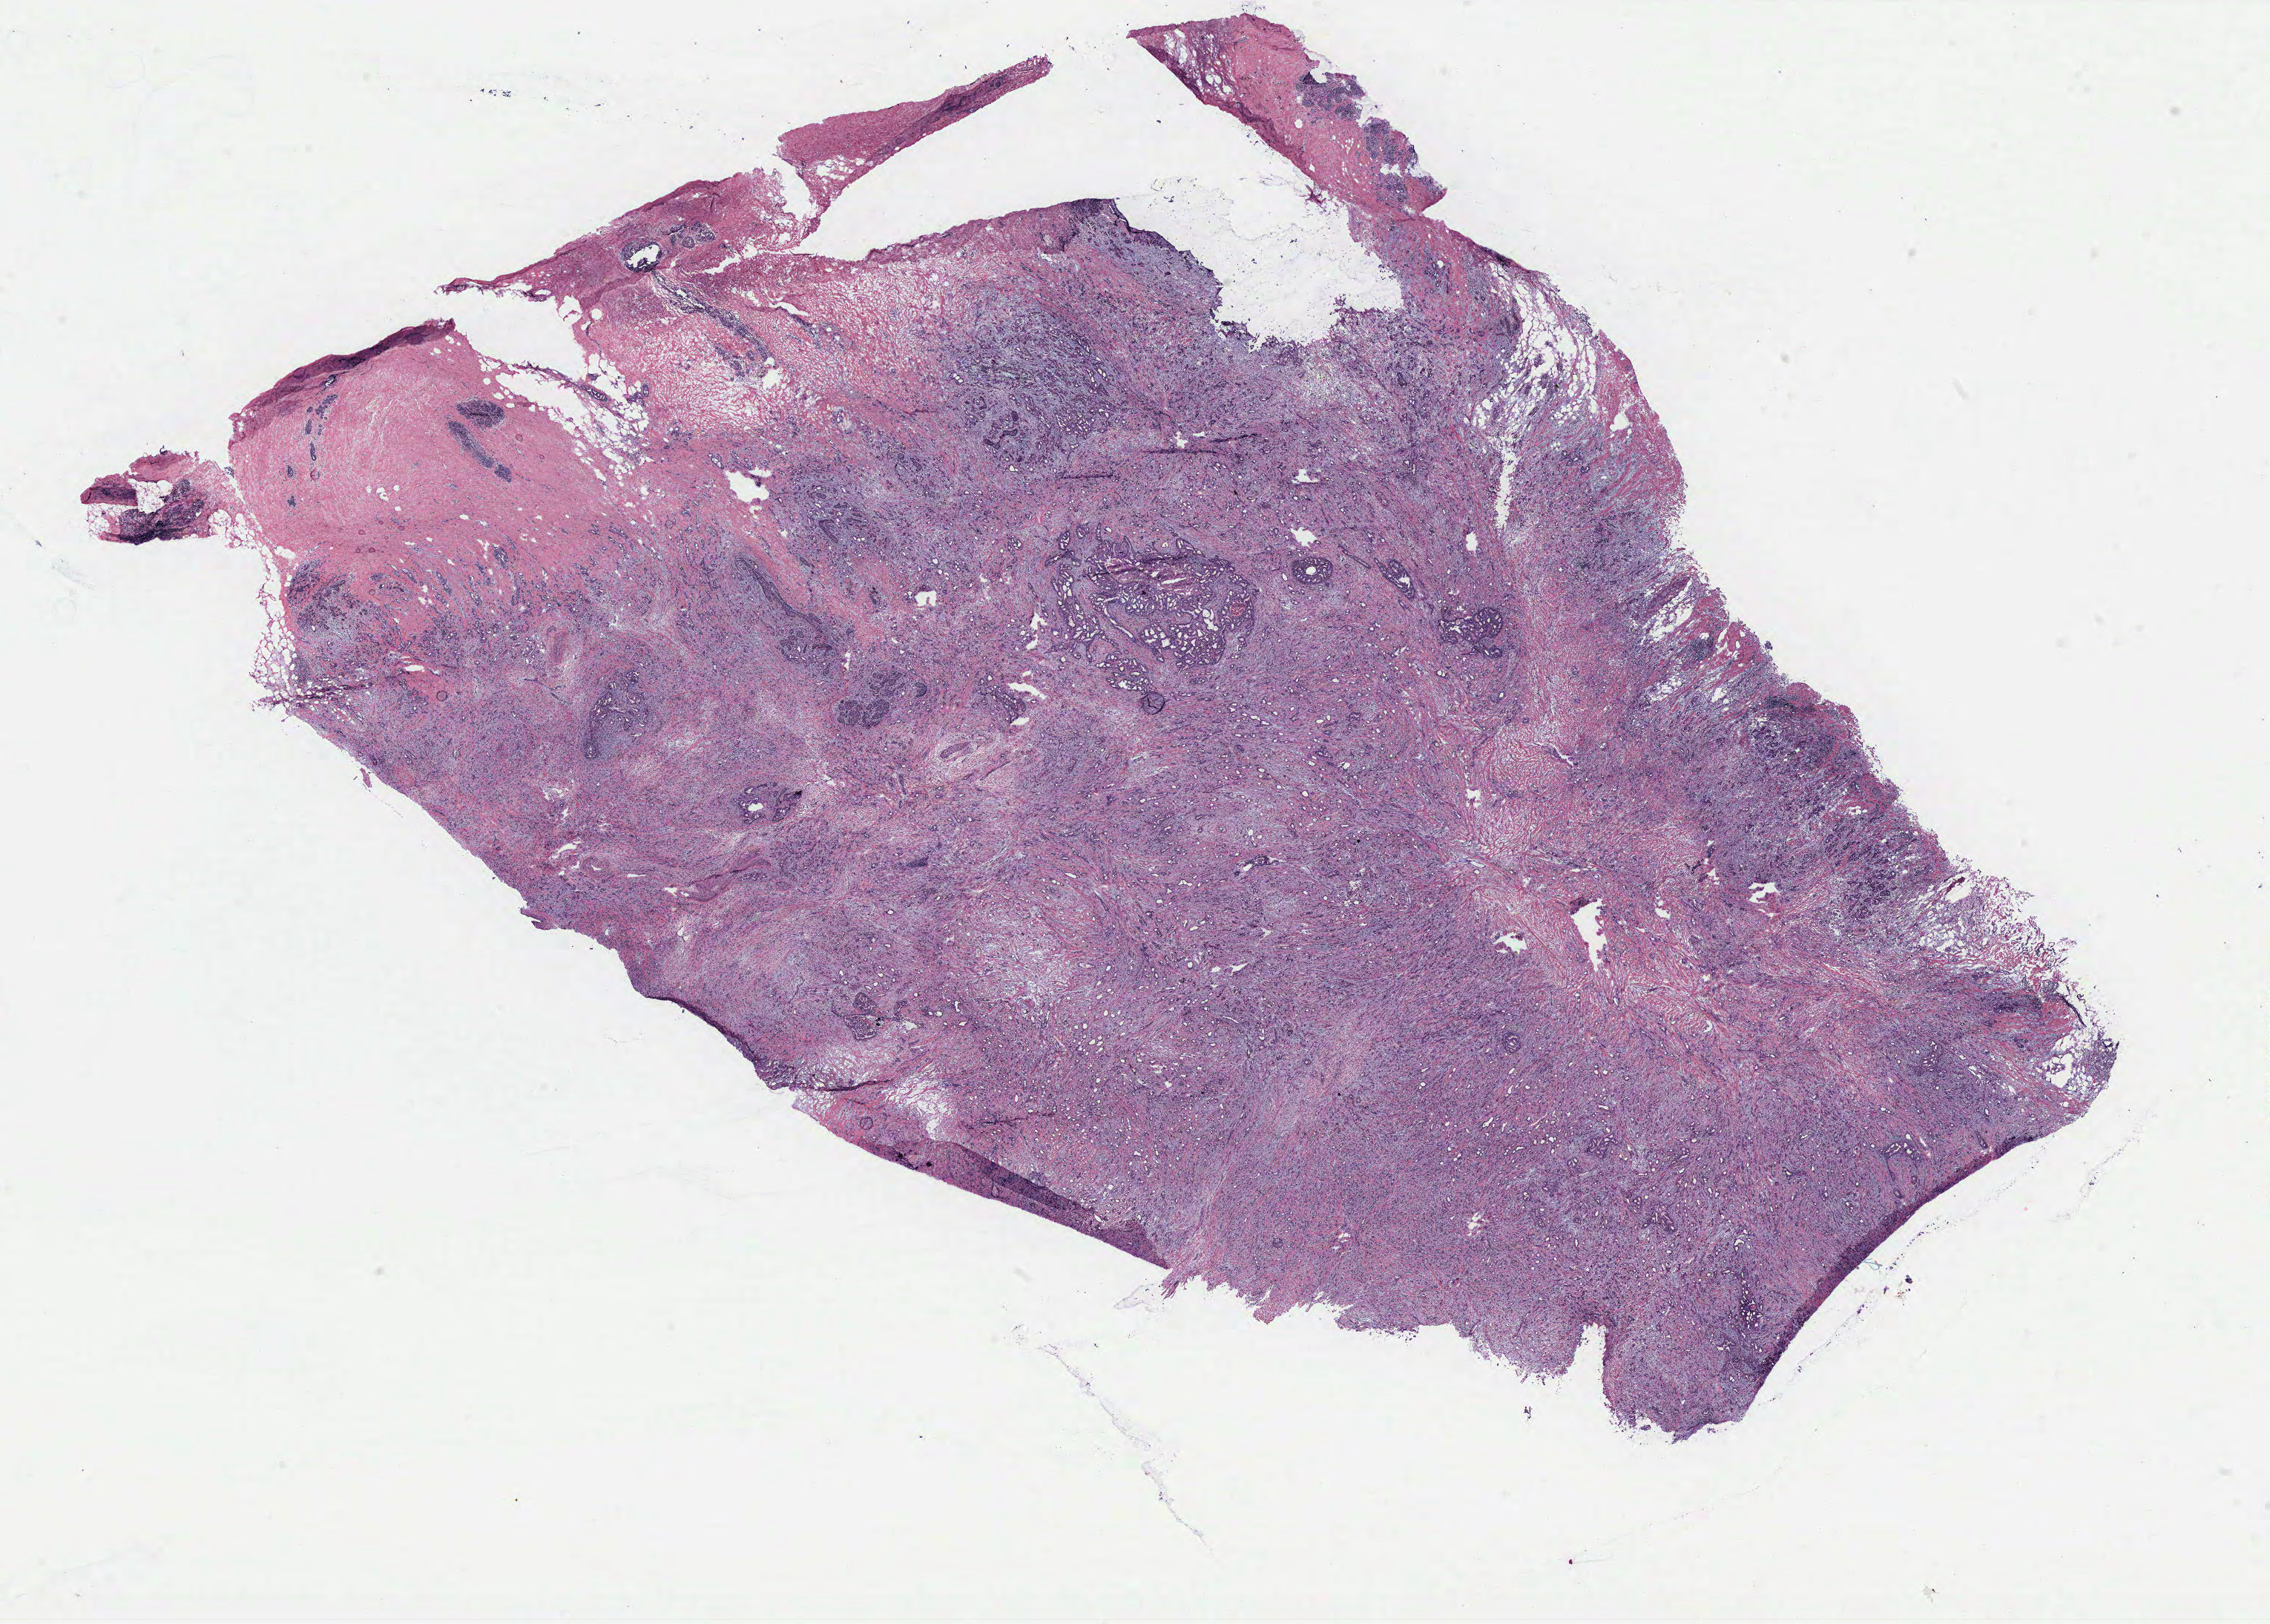
Digitized H&E tissue section (whole slide) — whole scanned area (about 24.5 x 17.5 mm) shown as a low-resolution overview. Breast, tissue type not recorded. 39-year-old female patient.
Patient diagnosis: Infiltrating duct carcinoma, NOS.